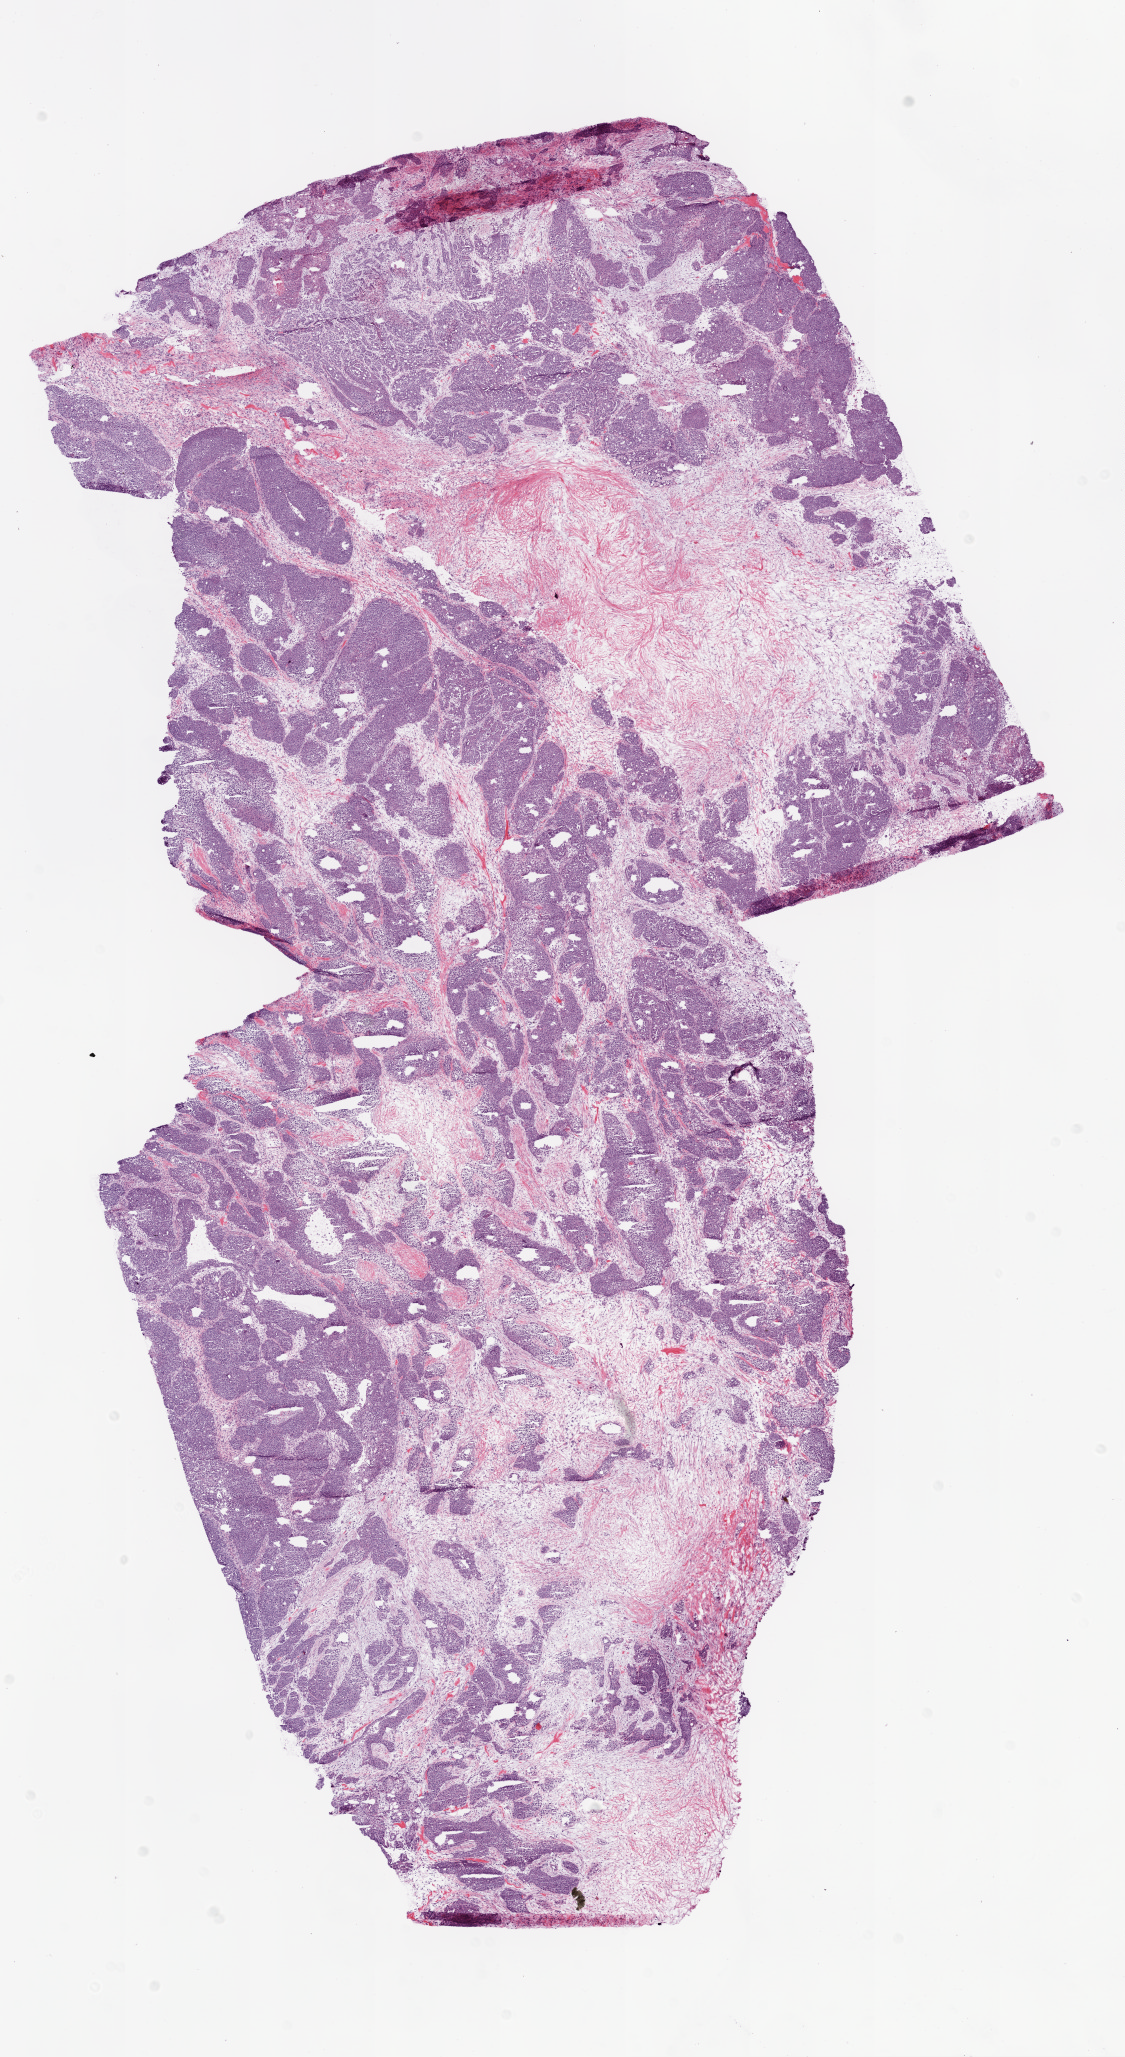
Digitized H&E-stained tissue section (whole slide) — a low-resolution overview of the entire scanned area, about 9.0 x 16.5 mm (slide scanned at 20x); frozen section from the bottom of the tissue portion; sample: primary tumour, ovary. Patient: female, age at initial diagnosis 52 years. Histologic grade: G3 (poorly differentiated). Slide review estimates, as recorded: tumour cells 95%, tumour nuclei 95%, normal cells 0%, stromal cells 5%, necrosis 0%.
Laterality: bilateral. Diagnosis: Serous cystadenocarcinoma, NOS. FIGO stage: IIIC.